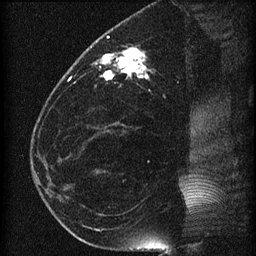
Breast MRI (dynamic contrast-enhanced), one sagittal slice. Position 26 of 60 along the scan axis. Dynamic contrast-enhanced series, image 2 of 4 at this slice position (ordered by acquisition). 1.5 T. TE 4.2 ms, TR 22.7 ms. 1.5 mm slice thickness. 256 × 256 image matrix, field of view 180 × 180 mm. Patient: female, 35 years. From the clinical record (not read from this slice): setting: breast cancer imaged before/during neoadjuvant chemotherapy; receptor status: HR-positive, HER2-negative.
Annotated regions visible in this slice (semi-automatically segmented with operator editing):
- analysis volume of interest (the breast-tissue region the enhancement analysis was run in; not a lesion): box from (x=69, y=27) to (x=199, y=112) px
- tumour enhancement mask (voxels above the 90 % enhancement threshold inside the analysis volume of interest): (x=69, y=46)–(x=145, y=81)